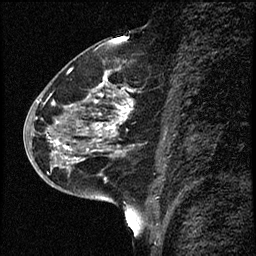
Breast MRI (dynamic contrast-enhanced), one sagittal slice. Position 31 of 68 along the scan axis. Dynamic contrast-enhanced study with each time point stored as its own series, time point 2 of 3 at this slice position (early post-contrast, ordered by acquisition time). 1.5 T. TE 4.2 ms, TR 17.6 ms. 2 mm slice thickness. 256 × 256 image matrix, field of view 200 × 200 mm. Patient: female, 52 years. From the clinical record (not read from this slice): setting: breast cancer imaged before/during neoadjuvant chemotherapy; receptor status: HER2-positive.
Structures marked on this image (semi-automatically segmented with operator editing):
- analysis volume of interest (the breast-tissue region the enhancement analysis was run in; not a lesion): box from (x=50, y=61) to (x=142, y=183) px
- tumour enhancement mask (voxels above the 100 % enhancement threshold inside the analysis volume of interest): (x=56, y=78)–(x=132, y=162)